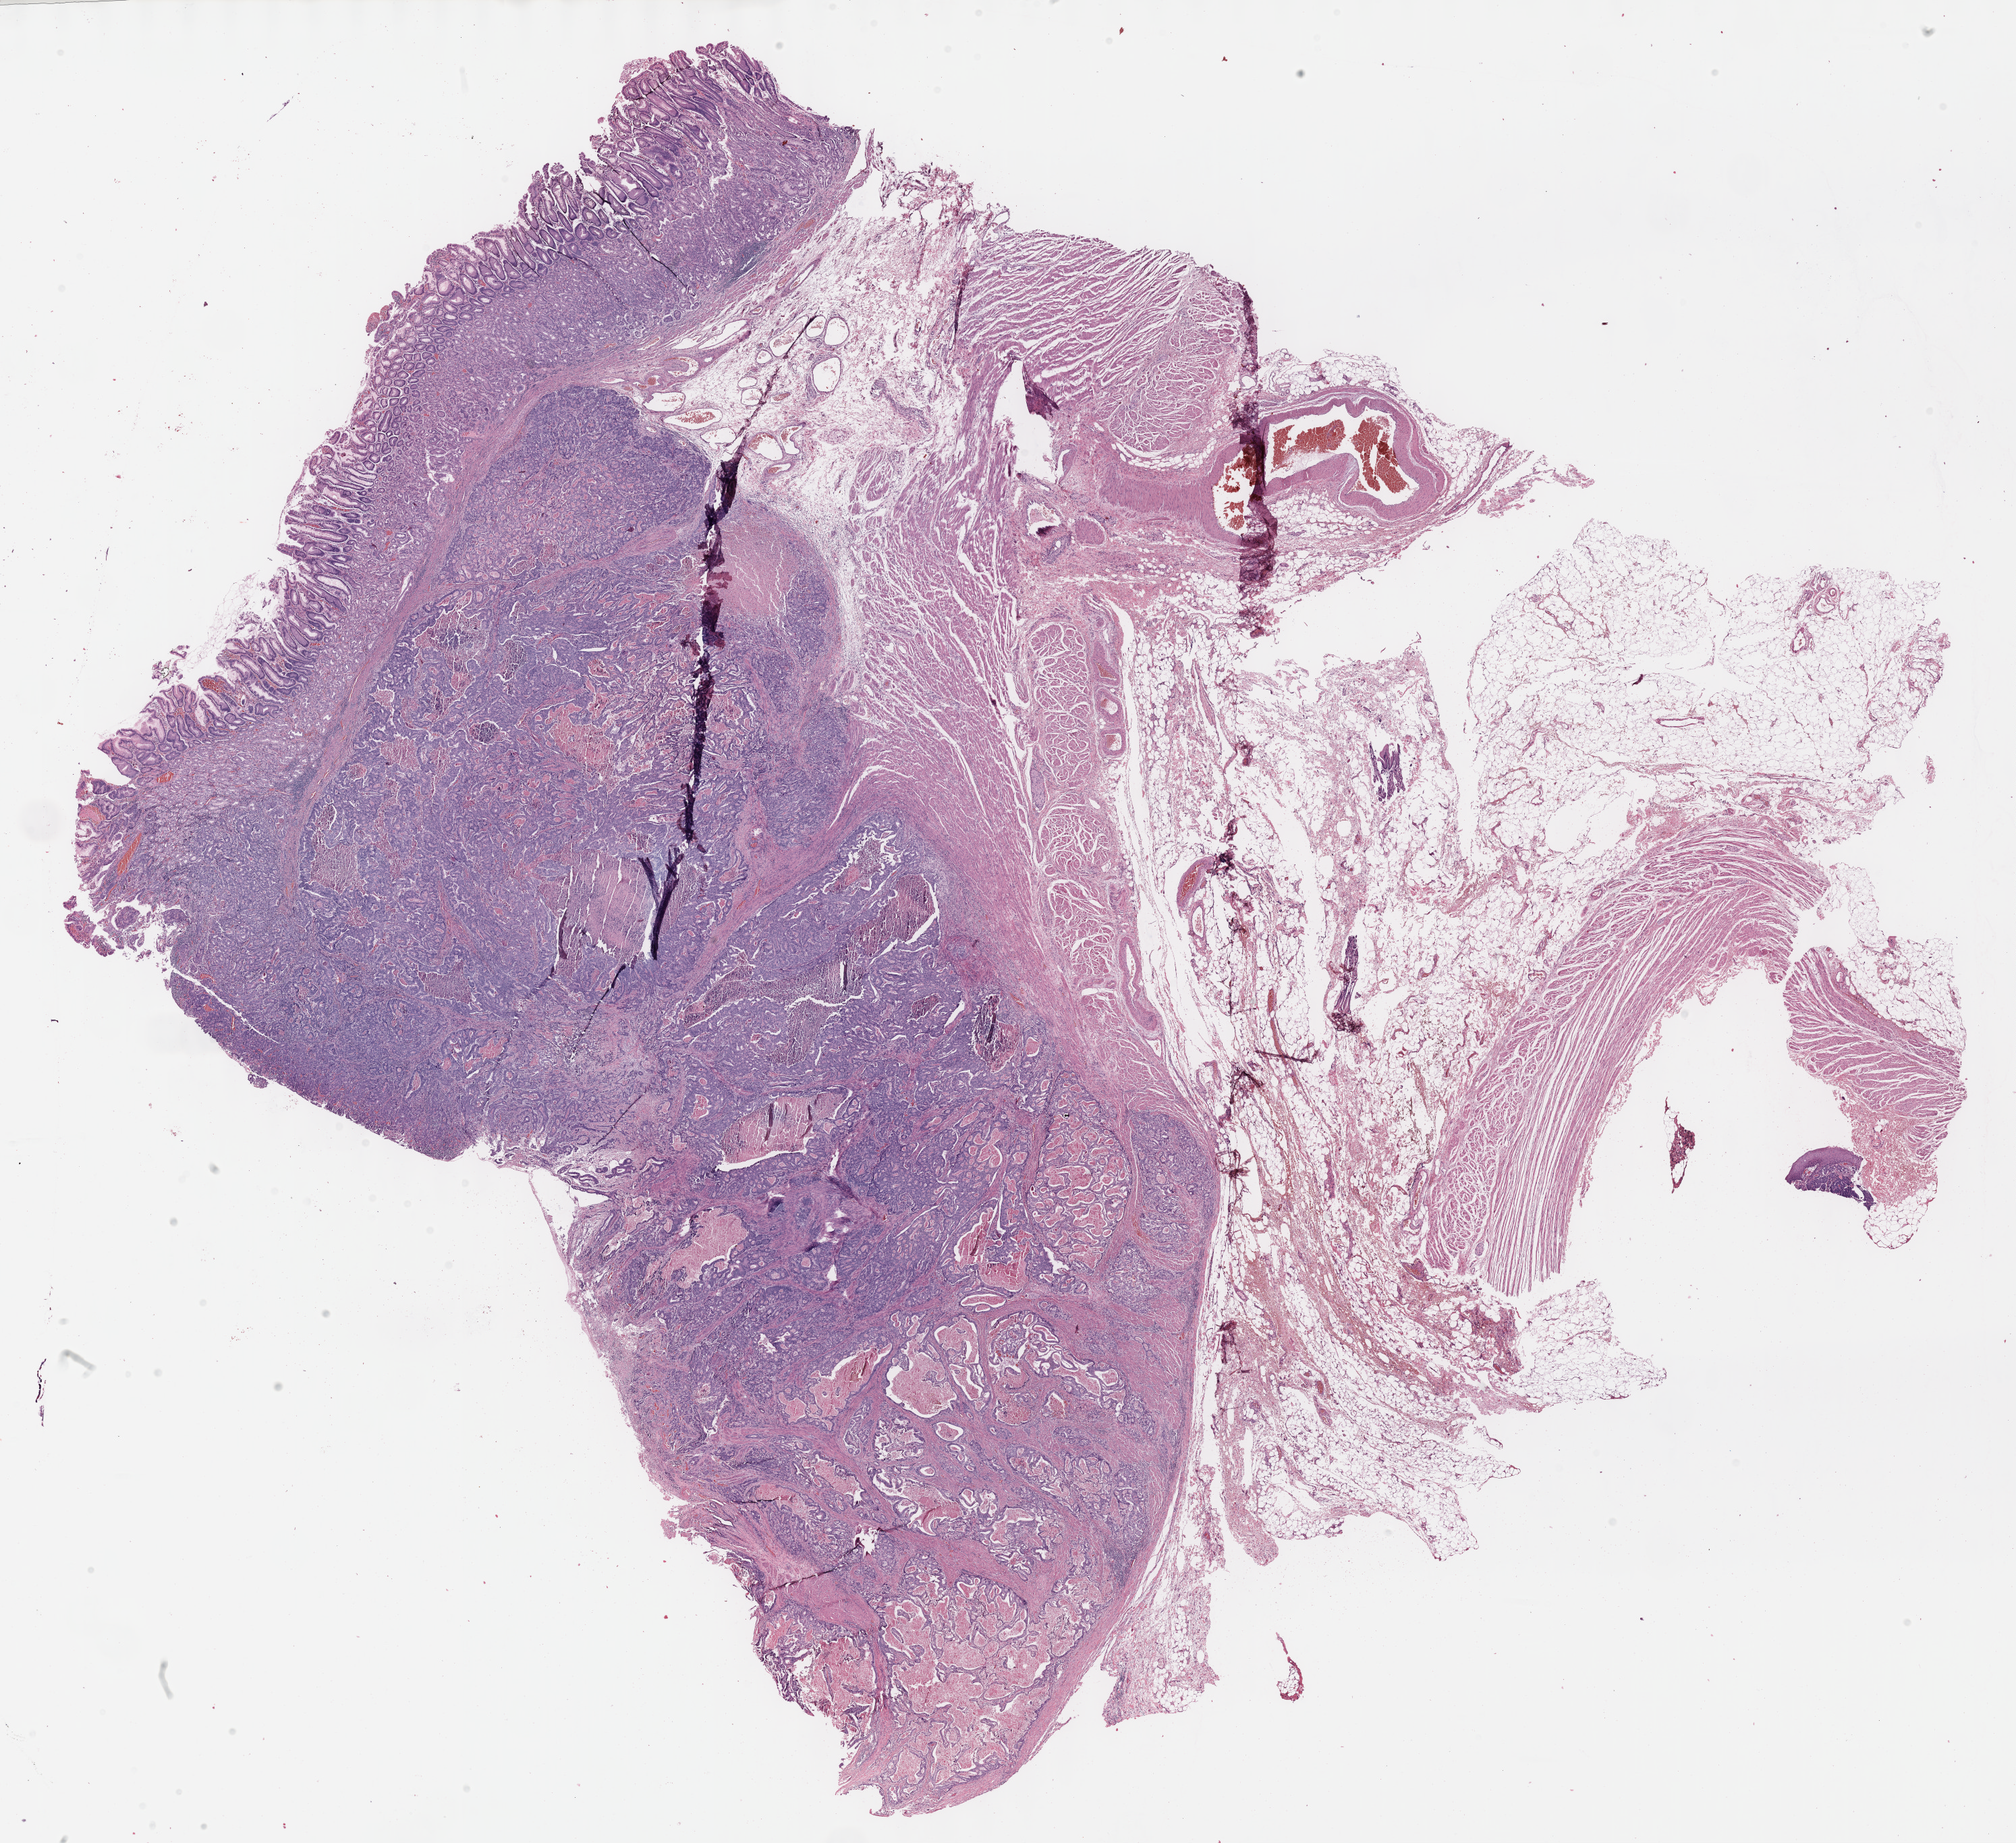
Digitized Hematoxylin and eosin (H&E) stained tissue section (whole slide) — low-resolution overview of the scanned area, about 24.1 x 22.1 mm. Formalin-fixed paraffin-embedded (FFPE) diagnostic section. Stomach, primary tumour sample. Patient: male, age at initial diagnosis 59 years. Histologic grade: G2 (moderately differentiated).
Histologic diagnosis: Tubular adenocarcinoma (cardia, NOS). AJCC pathologic stage: IV (7th edition).